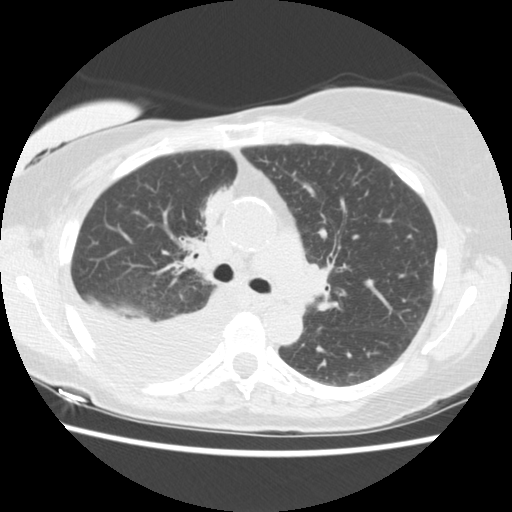
Low-dose screening chest CT, one axial slice. Reconstruction kernel STANDARD. Lung window (W 1500 / L -600 HU). 2.5 mm slice thickness. 512 × 512 image matrix, field of view 330 × 330 mm.
Structures marked on this image (outlined manually by an expert reader):
- lesion 1 (tumor, upper lobe of right lung): bounding box <205,189,232,225> (left, top, right, bottom; pixels)